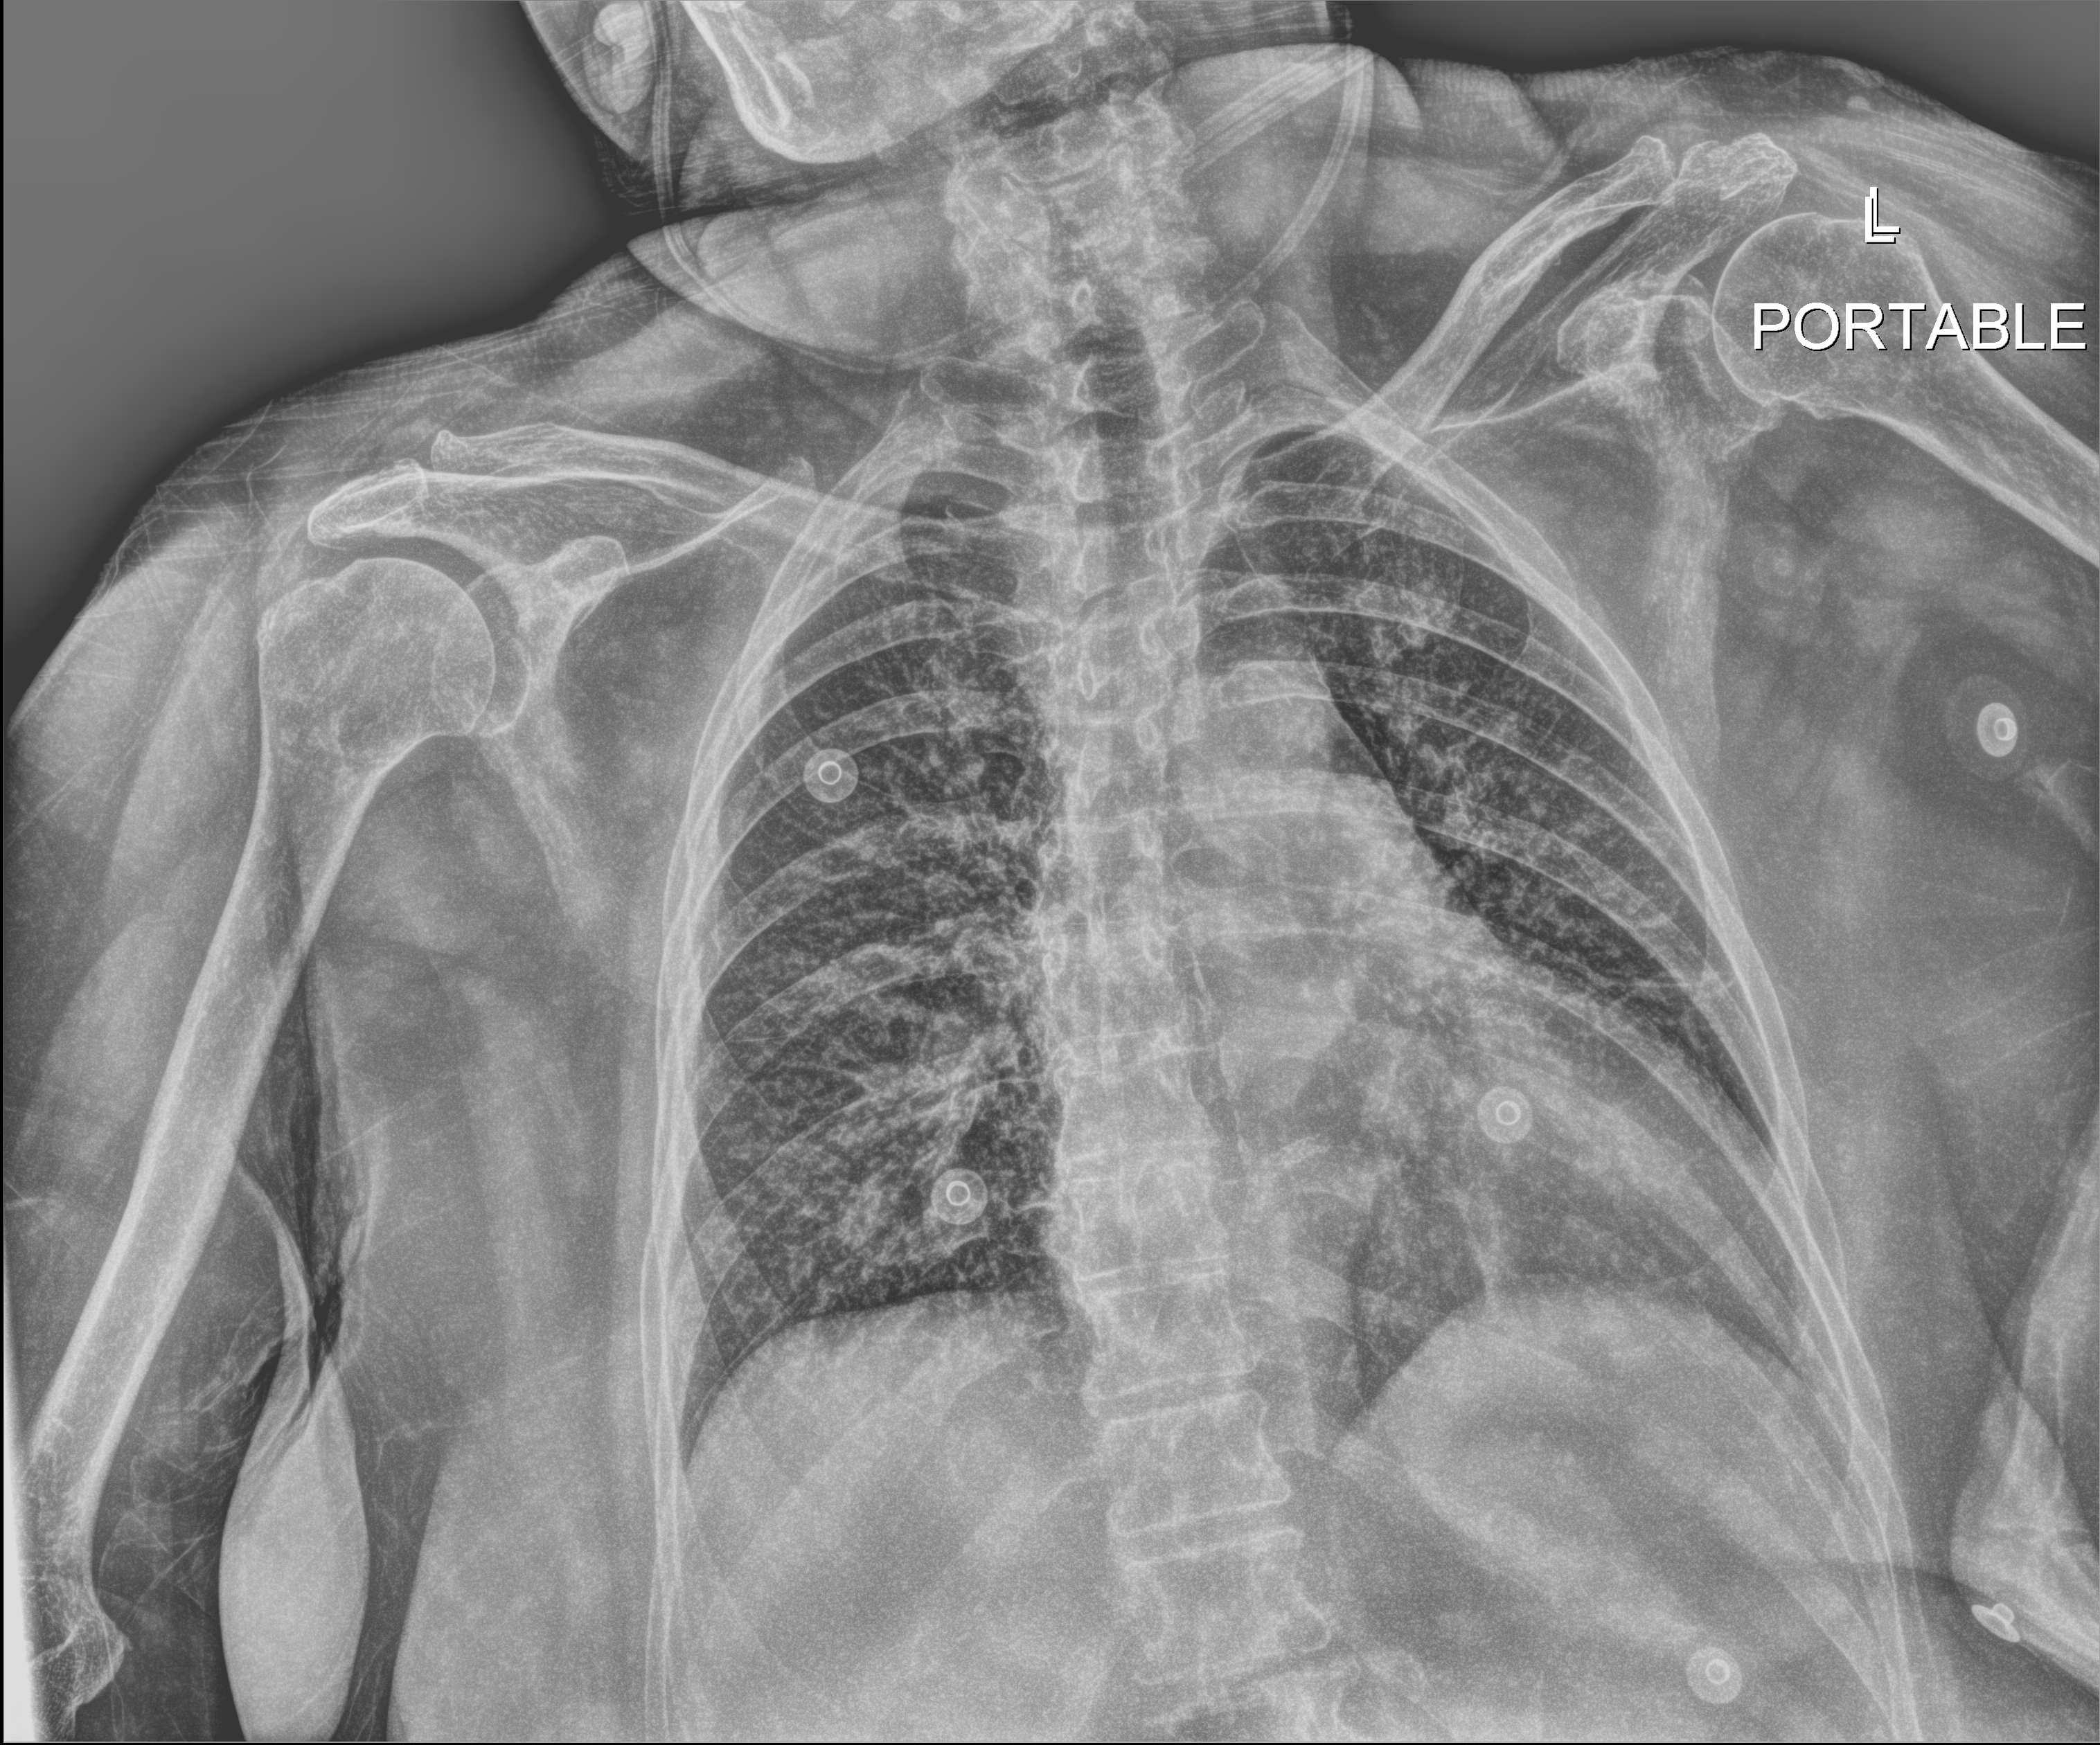
Chest radiograph (digital radiography); anteroposterior (AP) projection. Female patient hospitalised with COVID-19, age 75–90 years.
Hospital-stay facts (about this admission, not read from this image; timing relative to this image not recorded): mechanically ventilated during this hospital stay: no.